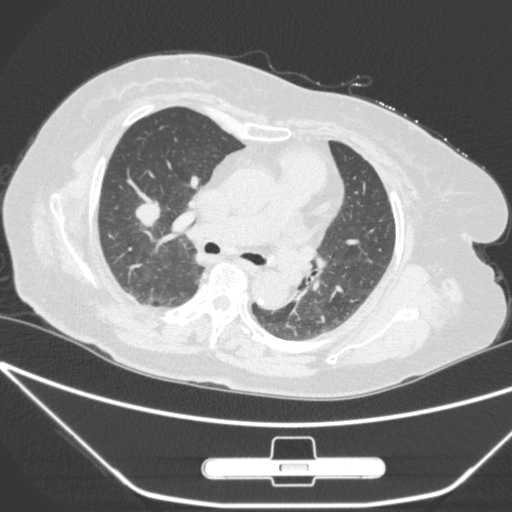
Chest CT, one axial slice; 120 kVp; lung window (W 1500 / L -600 HU); 512 × 512 image matrix, field of view 365 × 365 mm. Patient: female, 65 years. From the clinical record (not read from this slice): clinical TNM (as recorded): T1c N0 M0; histopathological grade: G3.
Annotated regions visible in this slice (bounding box drawn by a radiologist):
- lung tumour (recorded histology: adenocarcinoma): box from (x=133, y=195) to (x=169, y=236) px